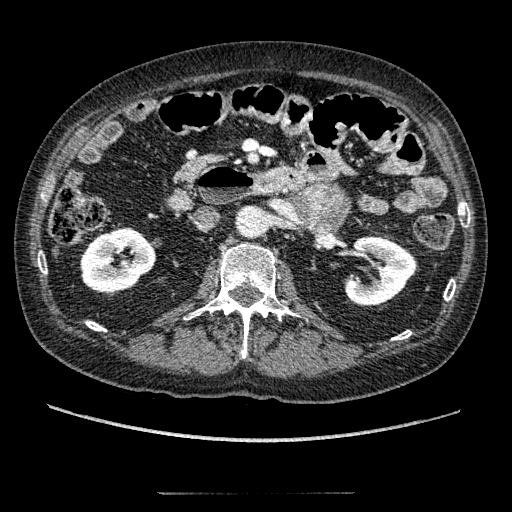
Contrast-enhanced abdominal CT, one axial slice. Position 85 of 274 along the scan axis. Reconstruction kernel STANDARD. 120 kVp. Soft-tissue window (W 400 / L 40 HU). 1.25 mm slice thickness. 512 × 512 image matrix. Patient: male, 69 years. From the clinical record (not read from this slice): diagnosis: adrenocortical carcinoma; tumour side: left adrenal; tumour size at pathology: 6.1 cm; Ki-67 index: 10 %; stage (as recorded): 3.
Structures marked on this image (semi-automatically segmented with operator editing):
- mass: bounding box [x1, y1, x2, y2] px = [297, 186, 349, 226]